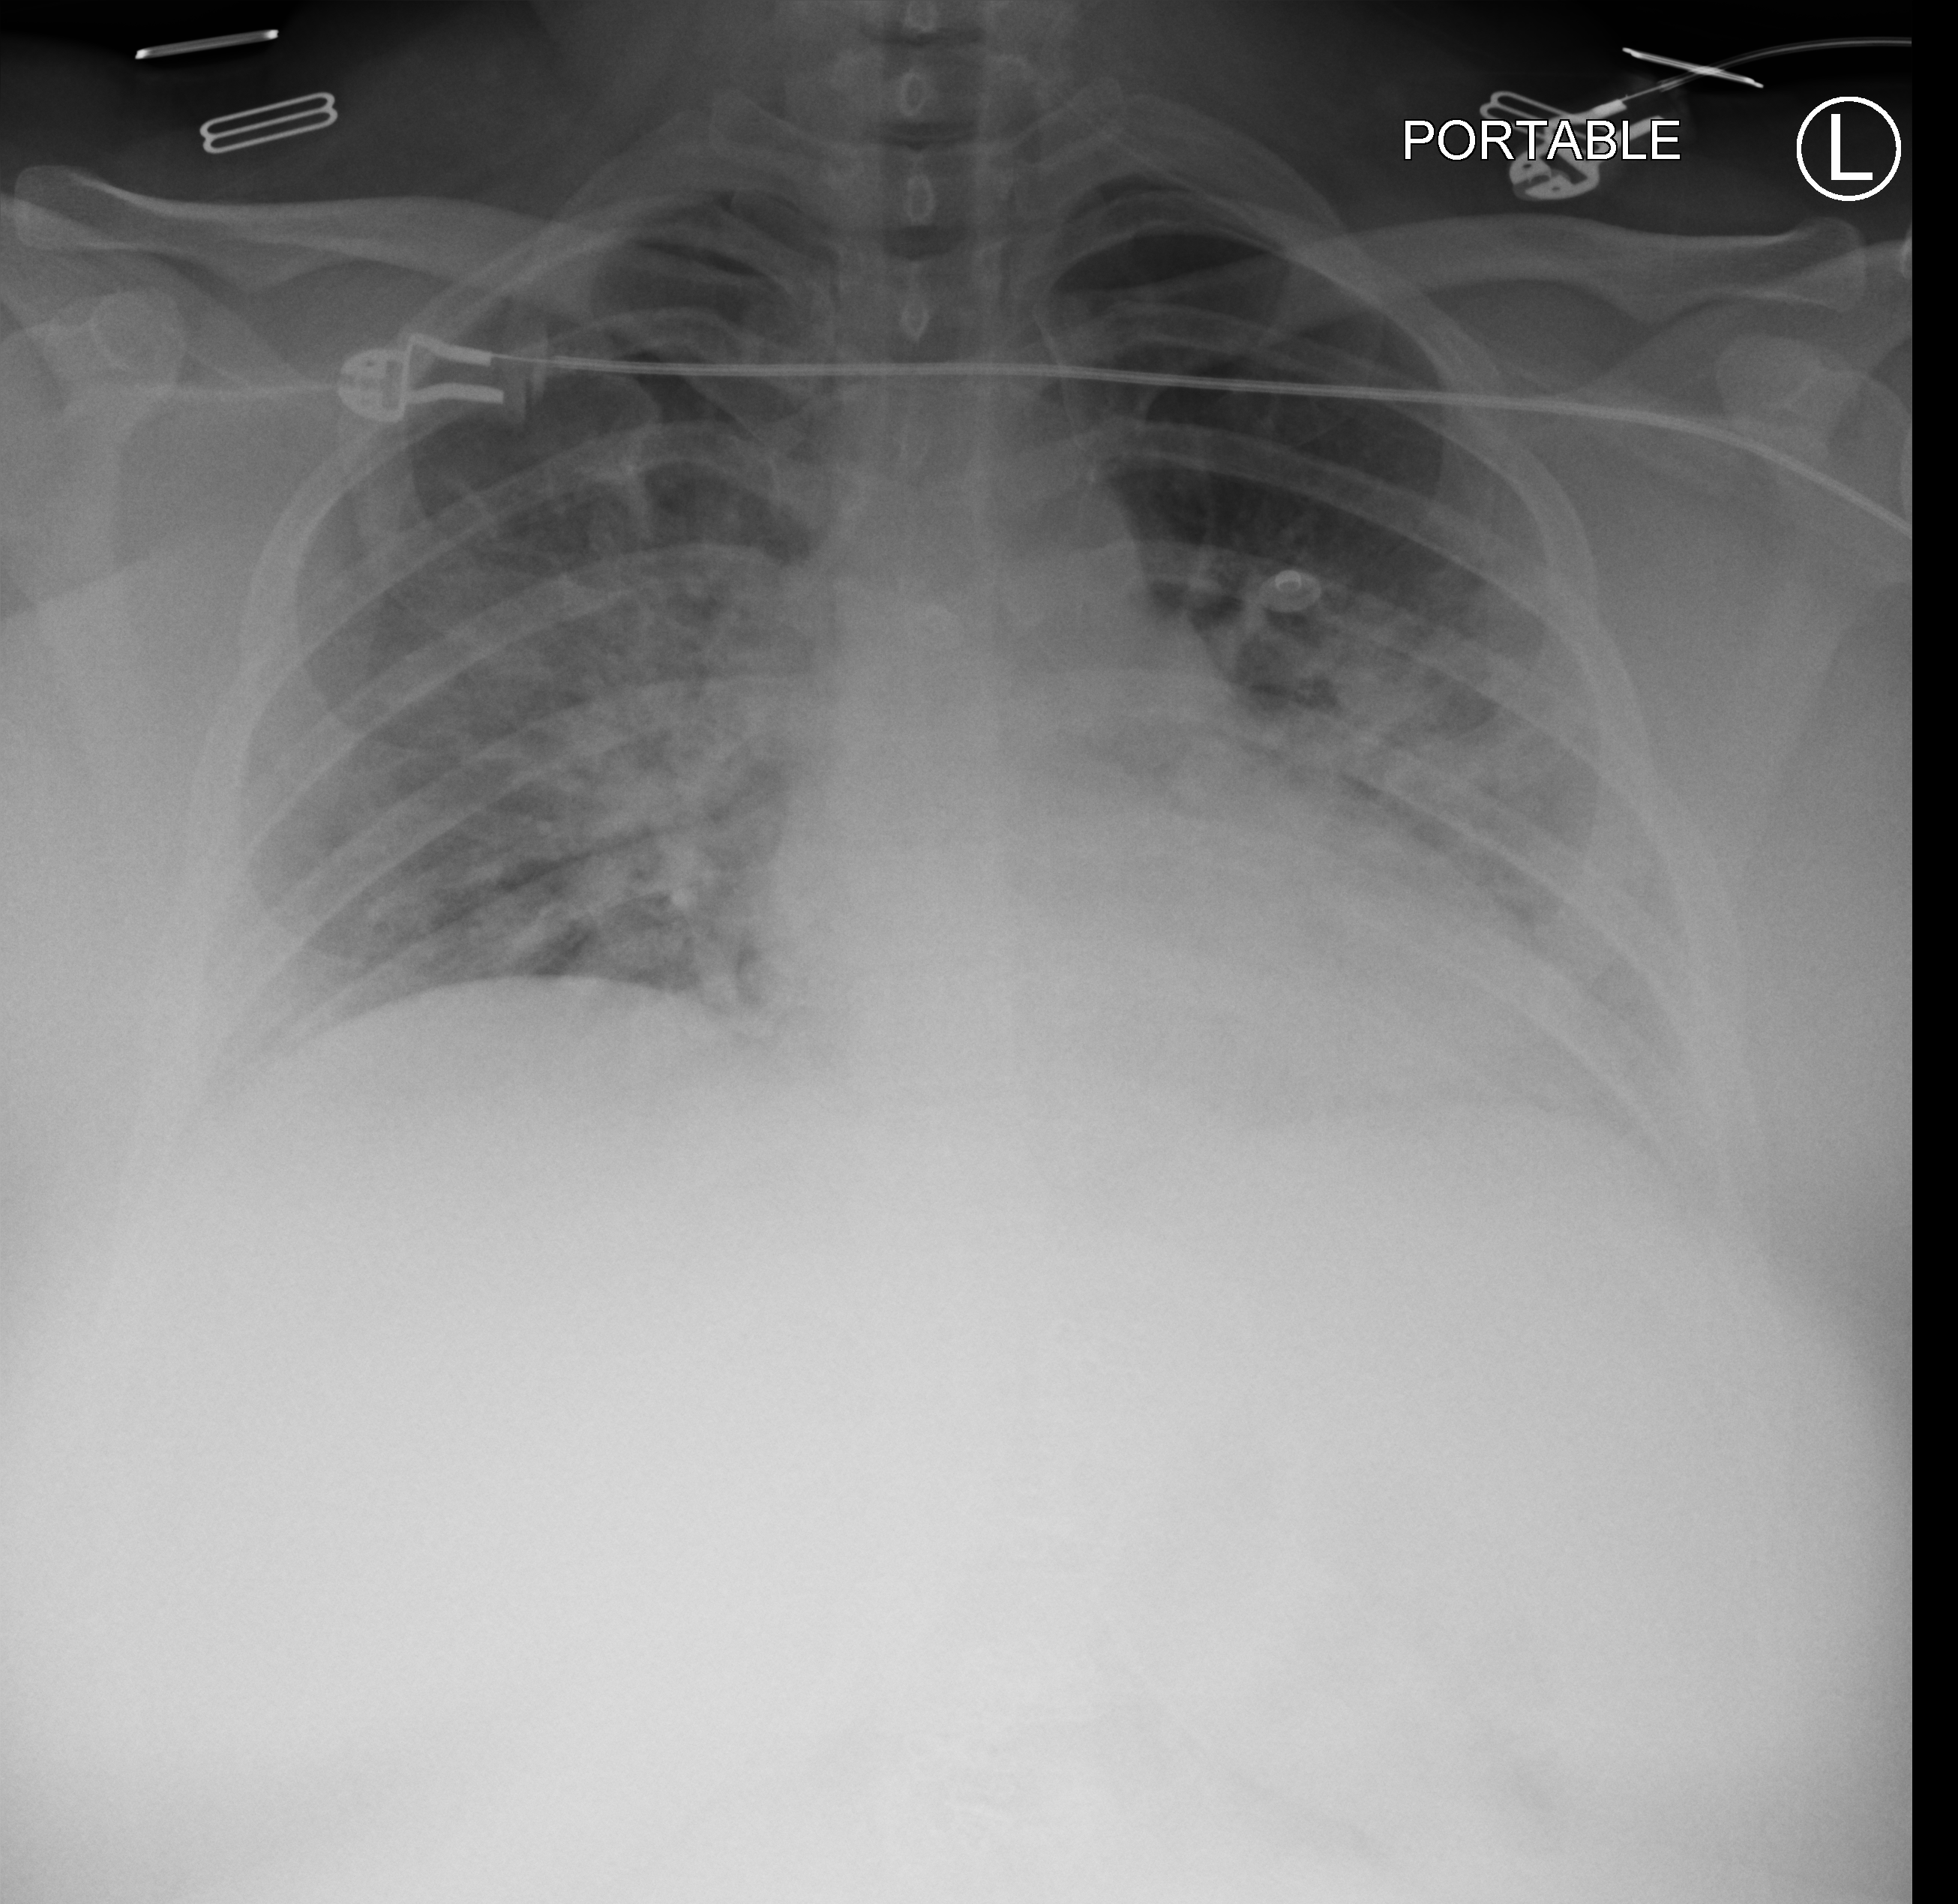
Bedside chest radiograph (computed radiography). Female patient hospitalised with COVID-19, age 18–59 years.
From the hospital-stay record, not from the radiograph (when in the stay this image was taken is not recorded): chronic kidney disease (admission record): no; mechanically ventilated during this hospital stay: no; admitted to intensive care during this hospital stay: no.